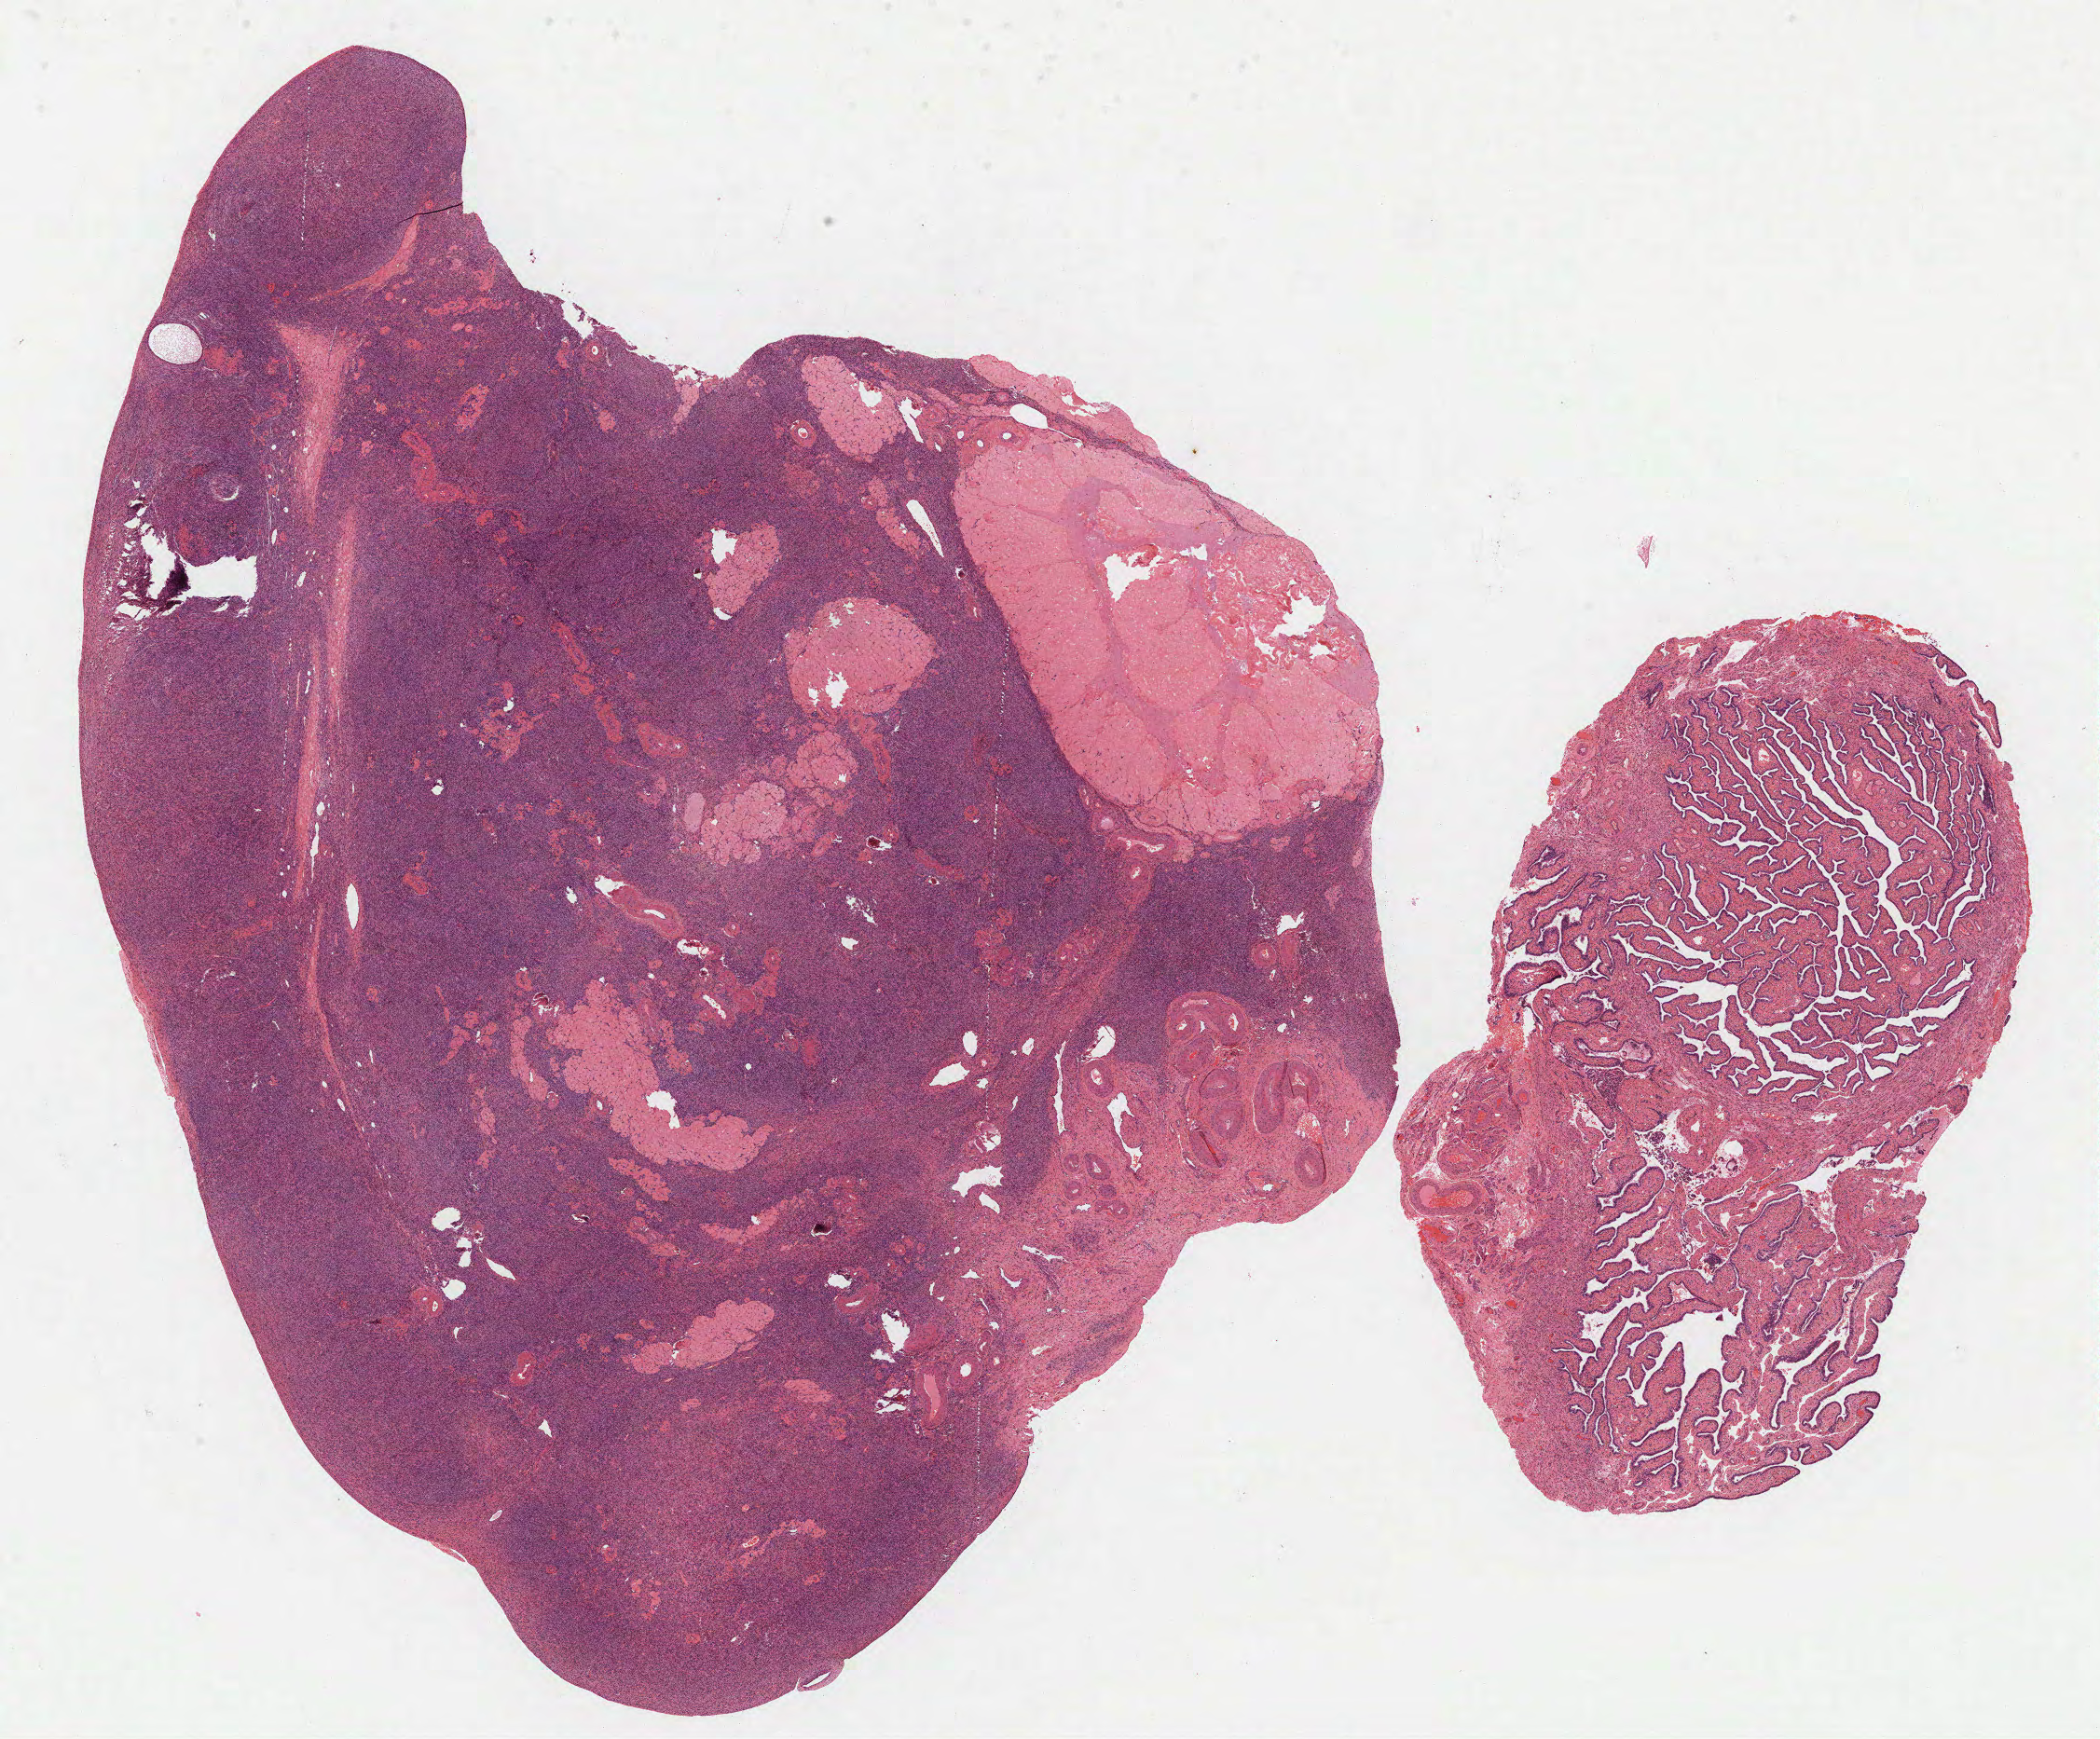
Digitized Hematoxylin and eosin (H&E) stained tissue section (whole slide) — whole scanned area (about 18.1 x 15.0 mm, from a 40x scan) shown as a low-resolution overview; formalin-fixed paraffin-embedded (FFPE) diagnostic section; sample: primary tumour, uterus. Female, age 58 years at initial diagnosis. Histologic grade: G3 (poorly differentiated).
FIGO stage: IB. Diagnosis: Endometrioid adenocarcinoma, NOS.